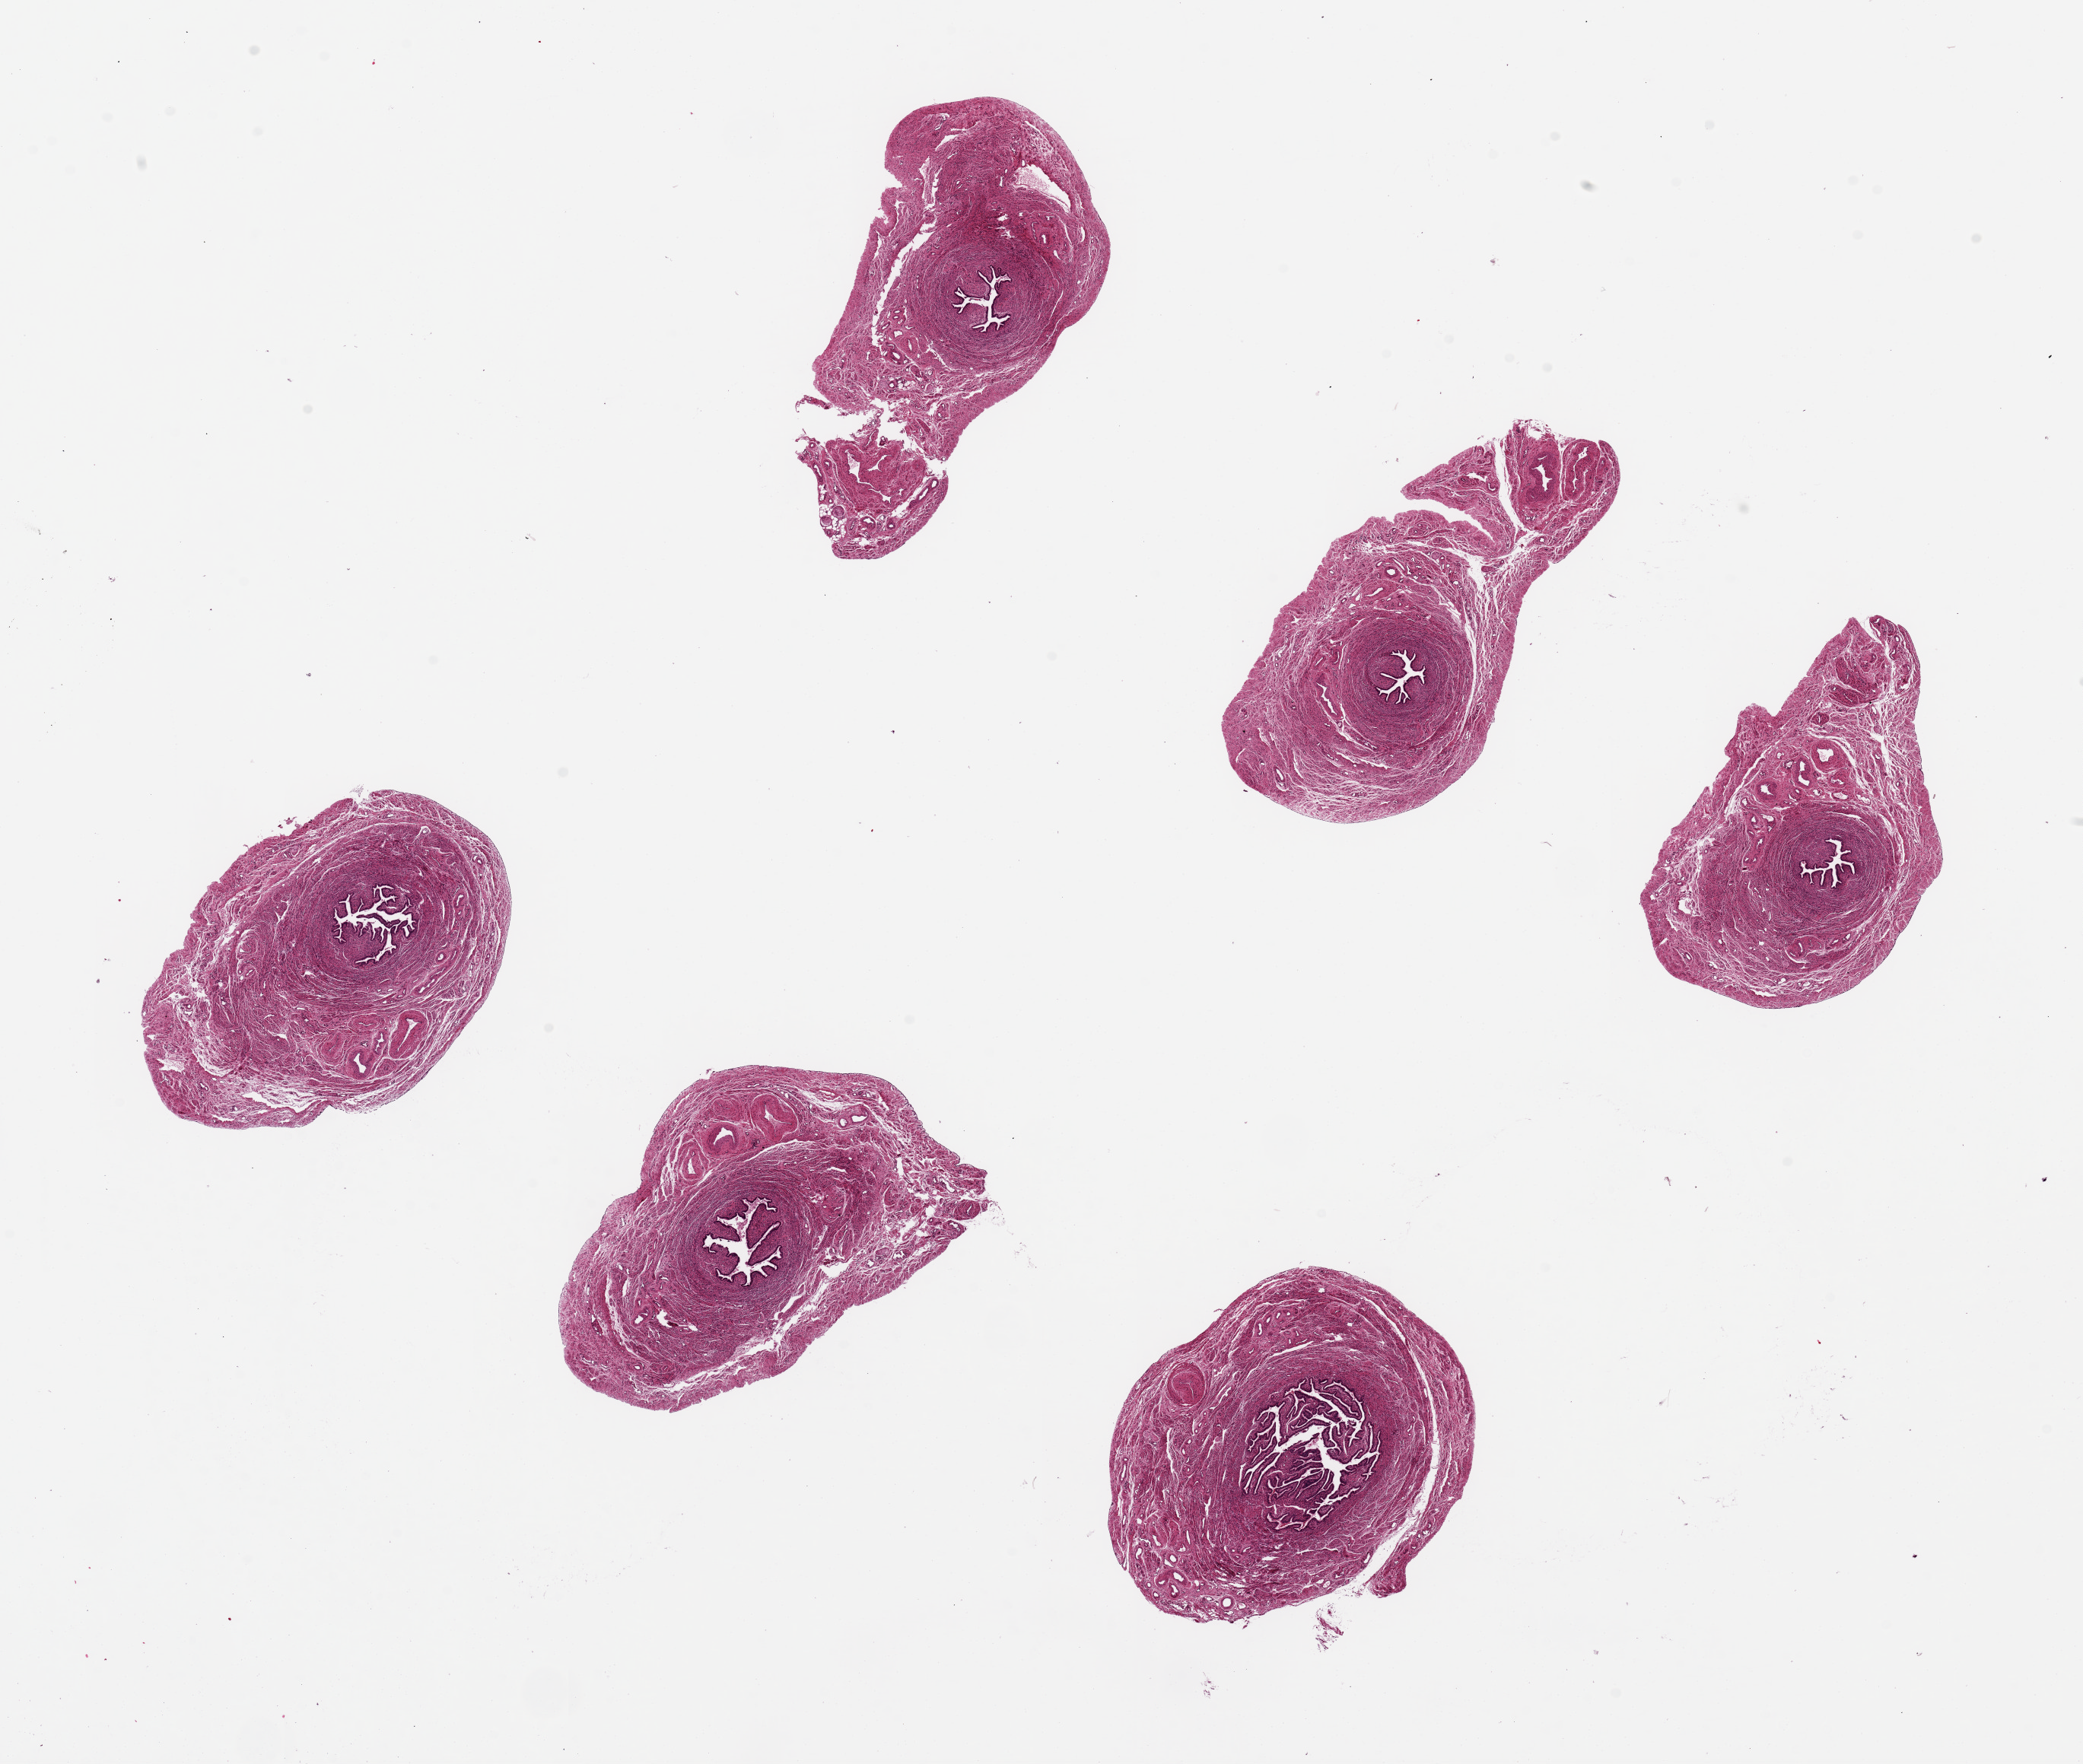
Whole-slide image, H&E stain, brightfield — shown as a low-resolution overview of the whole scanned area (about 21.7 x 18.3 mm); PAXgene-fixed paraffin-embedded (PFPE) section; target tissue: fallopian tube; tissue donor sample. Donor sex: female.
Reviewer comment on this tissue sample: 6 pieces ~3.5mm d, mucosa reasonably well perserved.